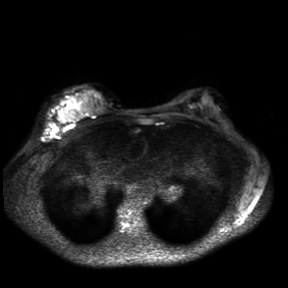
Breast MRI, one axial slice. Position 23 of 30 along the scan axis. Diffusion-weighted series; image 2 of 4 stored at this slice position (different b-values; order by instance number). 3 T. 4 mm slice thickness. 288 × 288 image matrix. Female patient.
Annotated regions visible in this slice (outlined manually by an expert reader):
- tumour on diffusion-weighted imaging: box from (x=60, y=111) to (x=75, y=121) px